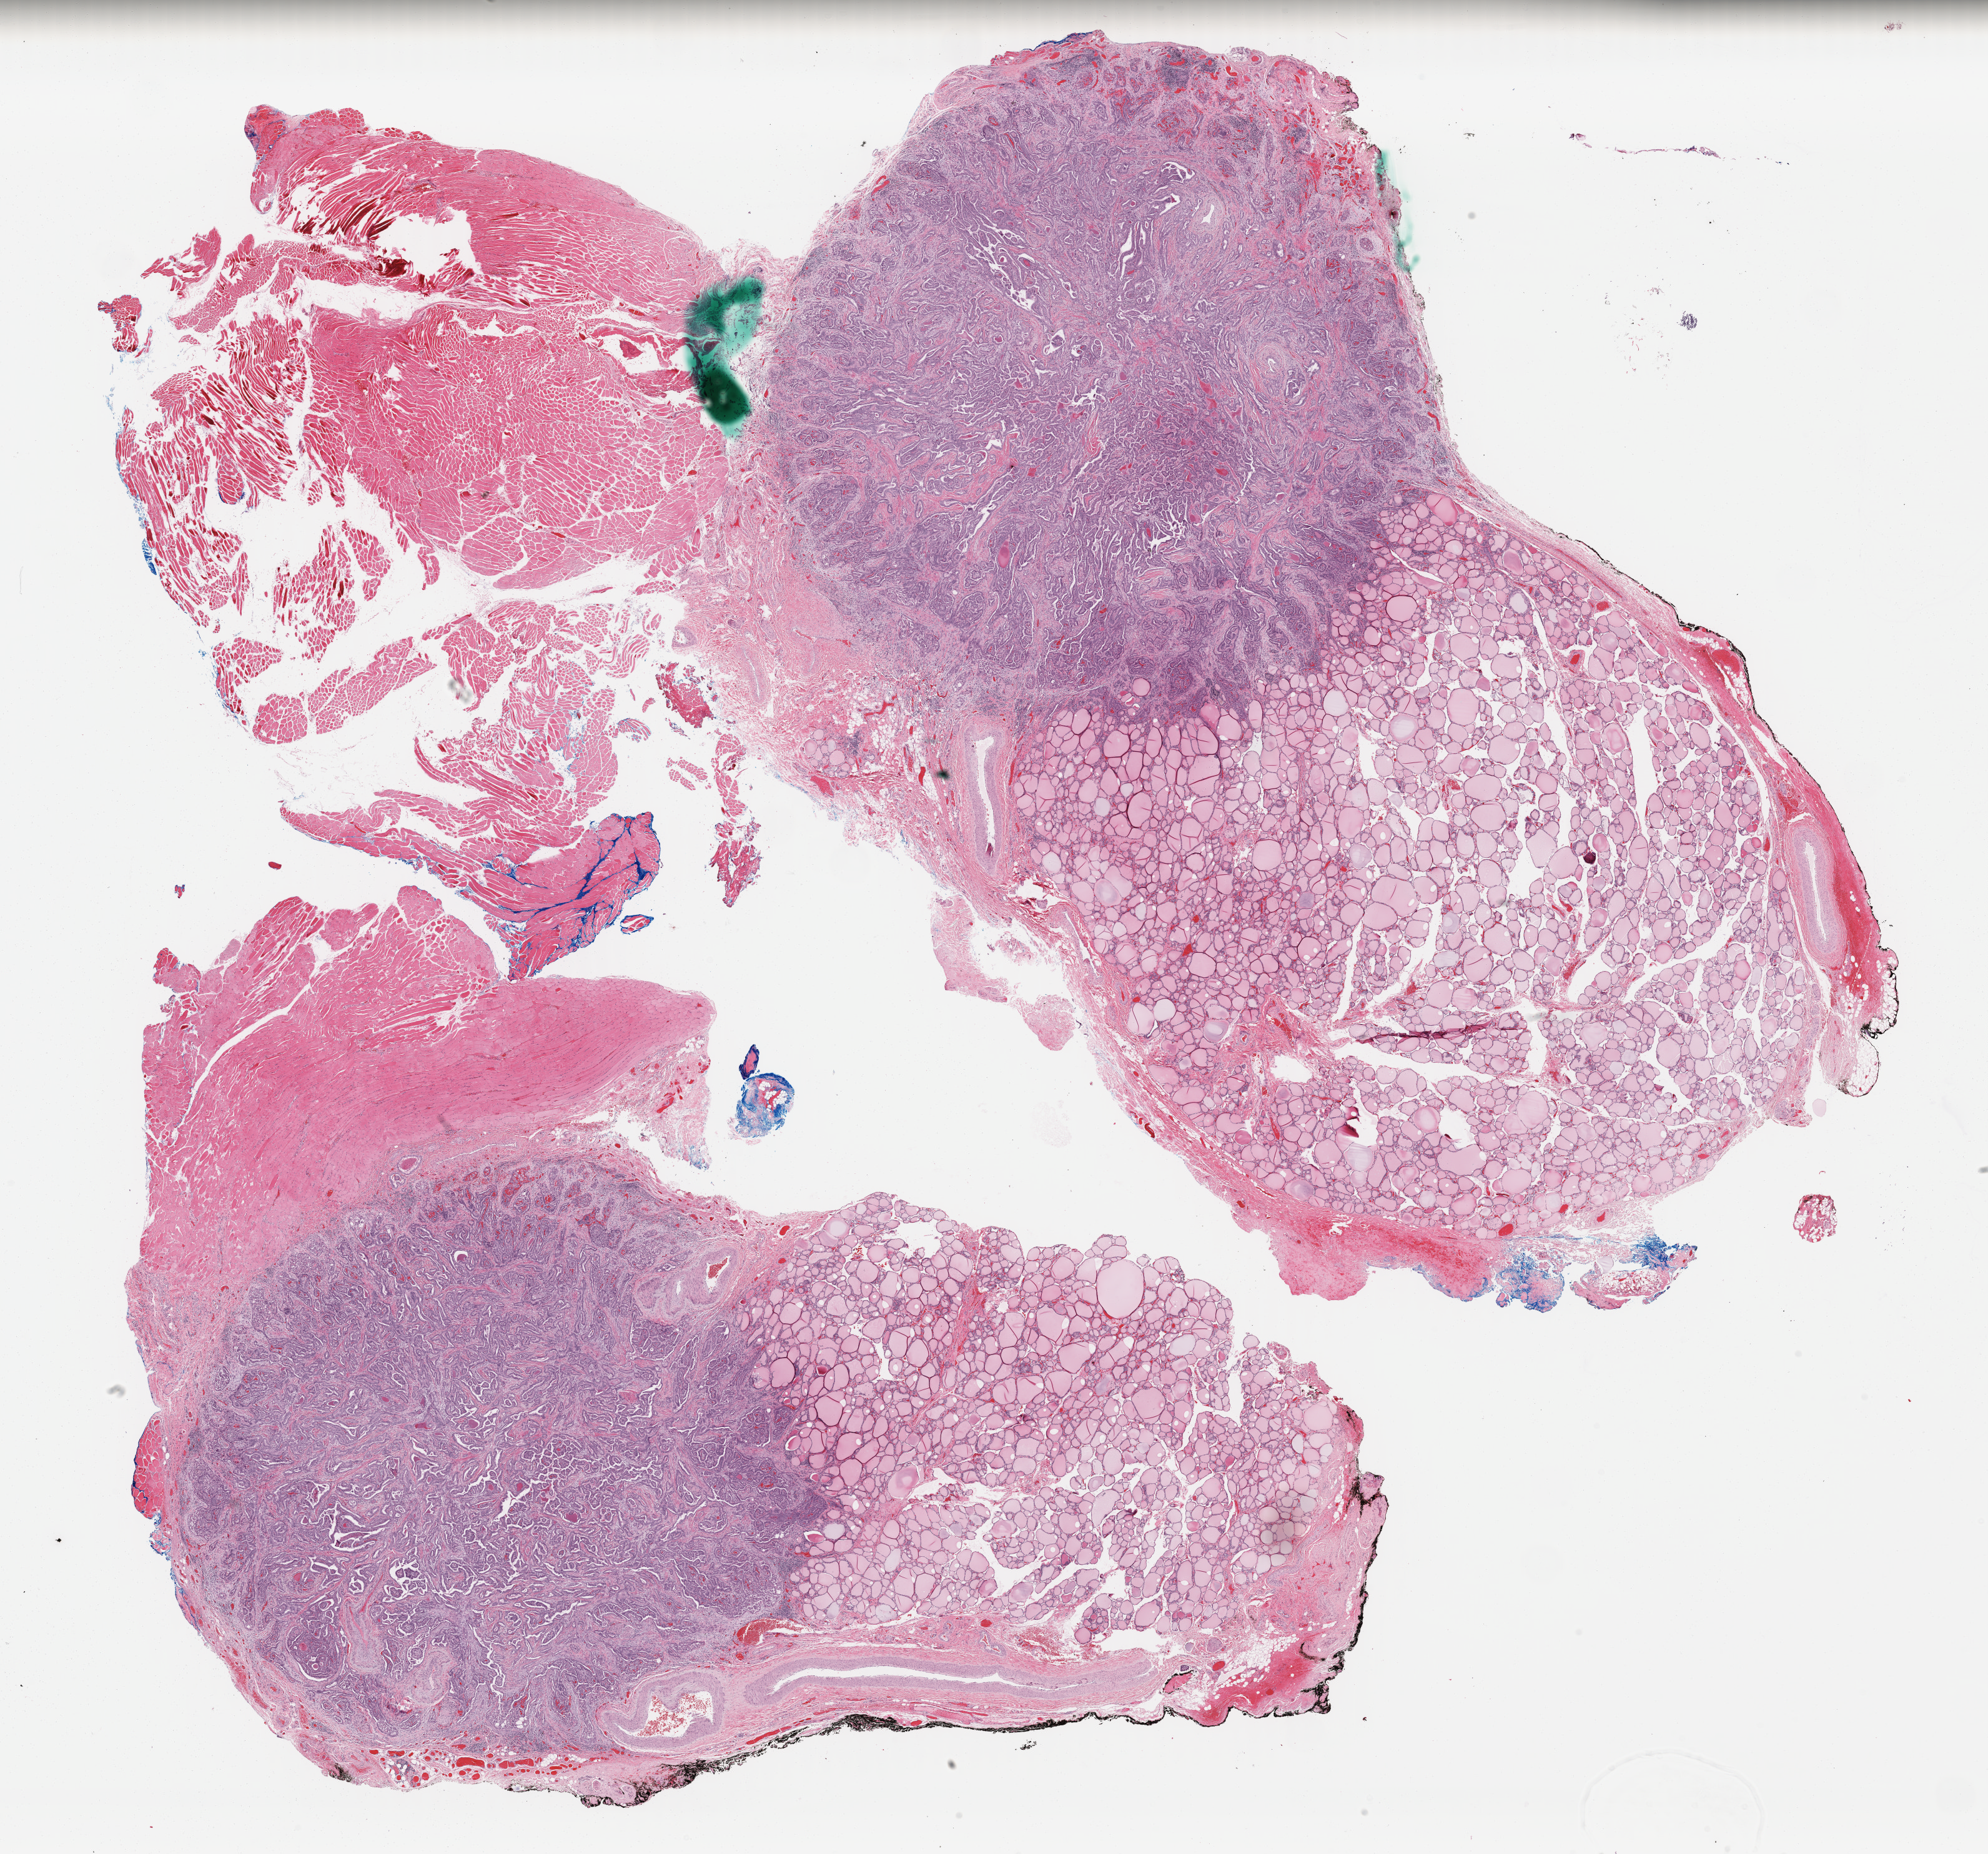
Digitized H&E-stained tissue section (whole slide) — low-resolution overview of the scanned area, about 25.1 x 23.4 mm, FFPE section, sample: primary tumour, thyroid. Patient: female, age at initial diagnosis 45 years.
AJCC pathologic stage: III (7th edition). Histologic diagnosis: Papillary carcinoma, columnar cell (thyroid gland).